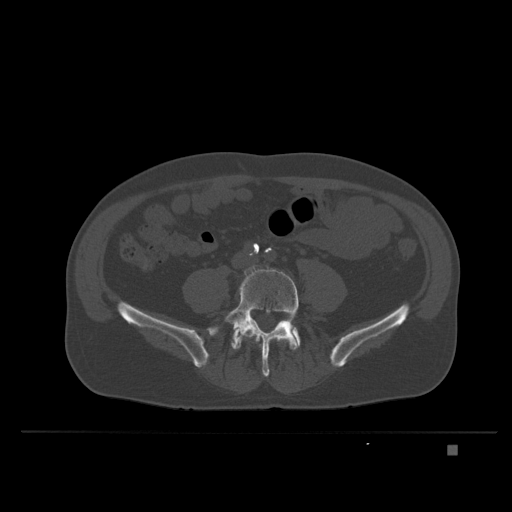
CT including the spine, one axial slice. Slice 58 of 435 in the series (ordered by position). Bone window (W 1800 / L 400 HU). 512 × 512 image matrix. Male patient, age 73 years. Case-level facts recorded for this patient, not image findings: primary cancer: skin.
Outlined on this slice (semi-automatic segmentation, software-assisted and operator-edited):
- L5 vertebra: bounding box (x1, y1, x2, y2) in pixels: (225, 265, 299, 377)